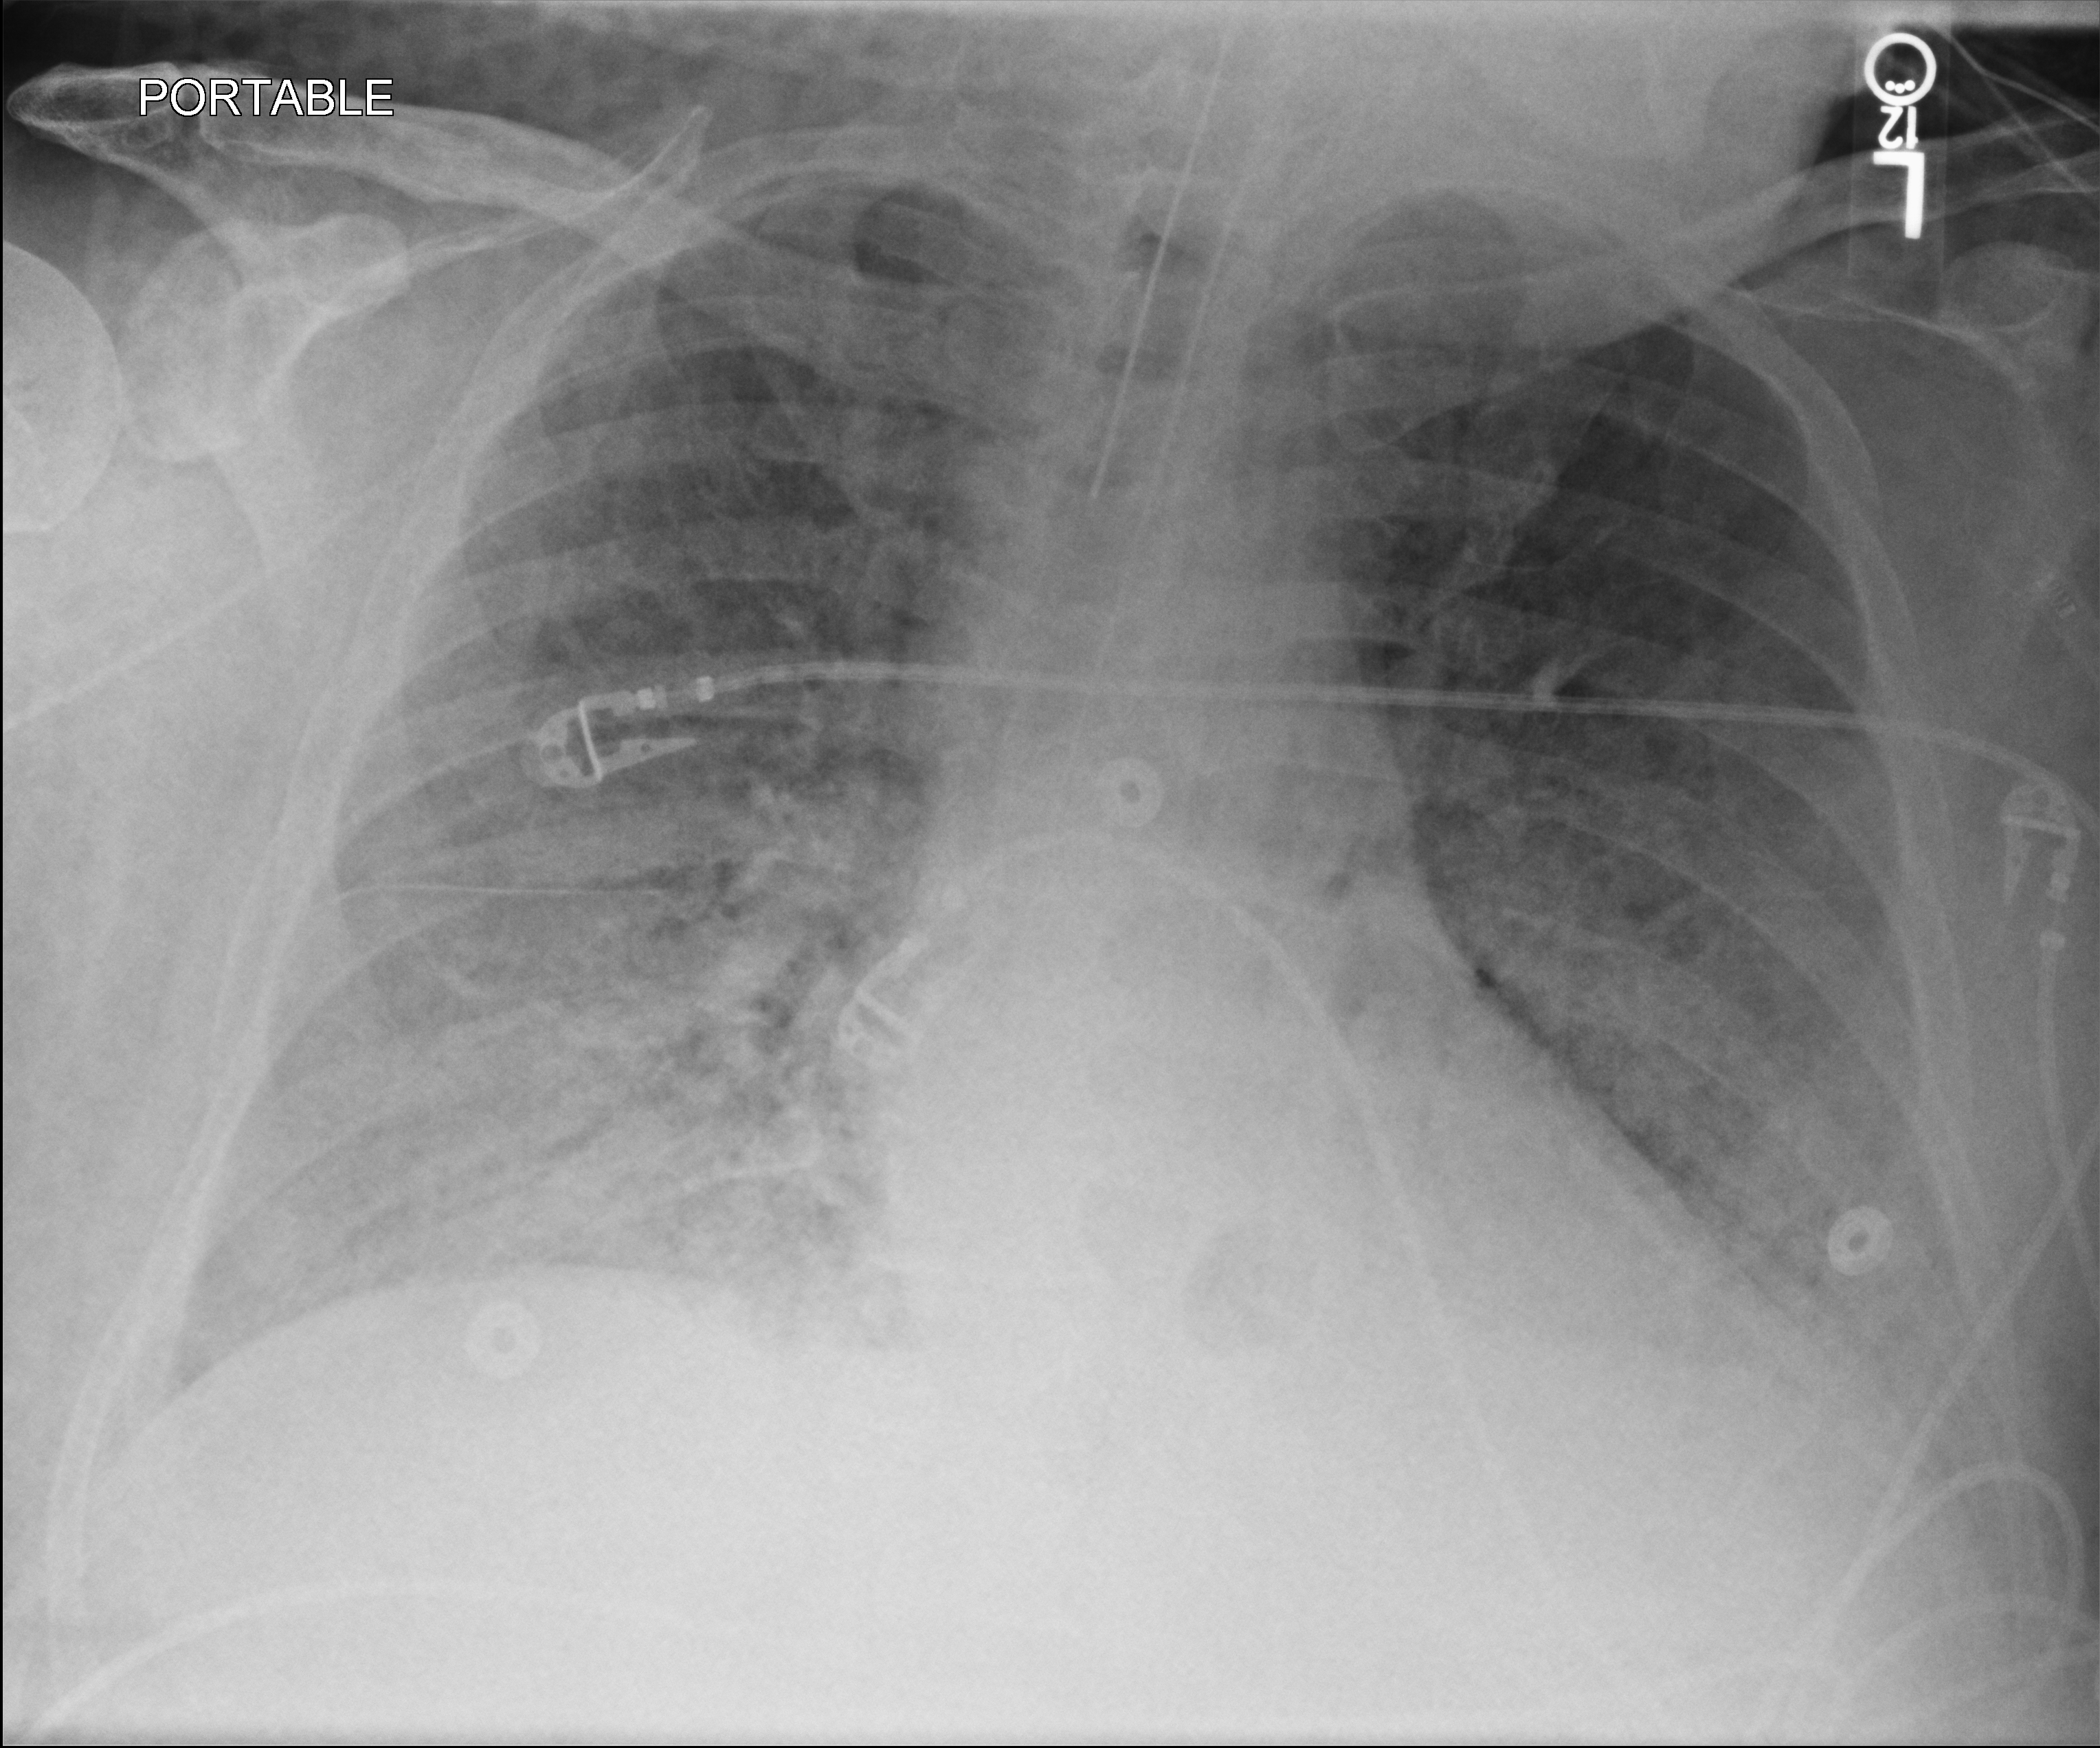
Chest X-ray (portable), anteroposterior (AP) projection. Patient hospitalised with COVID-19, aged 18–59 years.
From the hospital-stay record, not from the radiograph (when in the stay this image was taken is not recorded): chronic kidney disease (admission record): no; admitted to intensive care during this hospital stay: yes; mechanically ventilated during this hospital stay: yes.